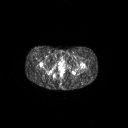
FDG PET of an extremity soft-tissue mass (from a PET/CT study), one axial slice; slice 34 of 267 in the series (ordered by position); 3.27 mm slice thickness; 128 × 128 image matrix, field of view 700 × 700 mm. Female patient, age 17 years. Case-level facts recorded for this patient, not image findings: histological type: epithelioid sarcoma; grade: intermediate; site of the primary tumour: right buttock.
Structures marked on this image (expert contour drawn on MRI and transferred to this co-registered scan by the dataset authors):
- gross tumour volume including surrounding oedema: bounding box (x1, y1, x2, y2) in pixels: (50, 71, 58, 80)
- gross tumour volume (mass): (51, 72, 56, 78)